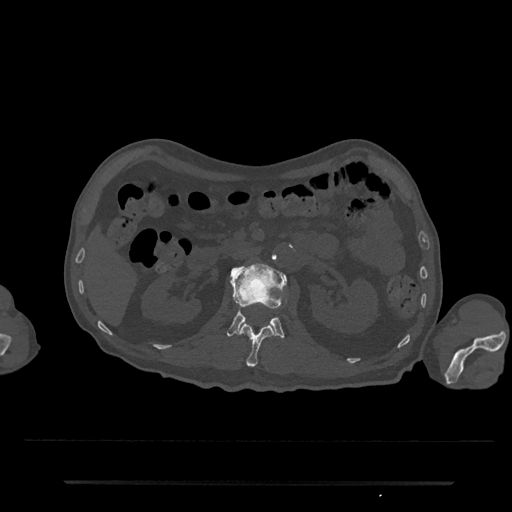
CT including the spine, one axial slice; position 96 of 797 along the scan axis; reconstruction kernel Br40s/3; bone window (W 1800 / L 400 HU); 0.5 mm slice thickness; 512 × 512 image matrix. Male patient, age 74 years. Case-level facts recorded for this patient, not image findings: primary cancer: prostate.
Annotated regions visible in this slice (semi-automatically segmented with operator editing):
- L1 vertebra: box from (x=237, y=322) to (x=275, y=367) px
- L2 vertebra: (x=227, y=263)–(x=286, y=337)